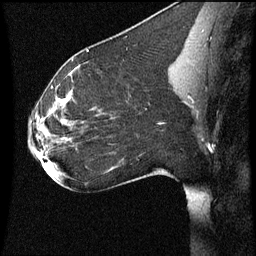
Breast MRI (dynamic contrast-enhanced), one sagittal slice; position 31 of 60 along the scan axis; dynamic contrast-enhanced series, image 2 of 3 at this slice position (ordered by acquisition); 1.5 T; TE 4.2 ms, TR 8.9 ms; 2 mm slice thickness; 256 × 256 image matrix, field of view 200 × 200 mm. Patient: female, 35 years. Case-level facts recorded for this patient, not image findings: setting: breast cancer imaged before/during neoadjuvant chemotherapy; receptor status: HER2-positive.
Annotated regions visible in this slice (semi-automatic segmentation, software-assisted and operator-edited):
- analysis volume of interest (the breast-tissue region the enhancement analysis was run in; not a lesion): bounding box [x1, y1, x2, y2] px = [27, 66, 177, 177]
- tumour enhancement mask (voxels above the 70 % enhancement threshold inside the analysis volume of interest): [42, 94, 72, 141]